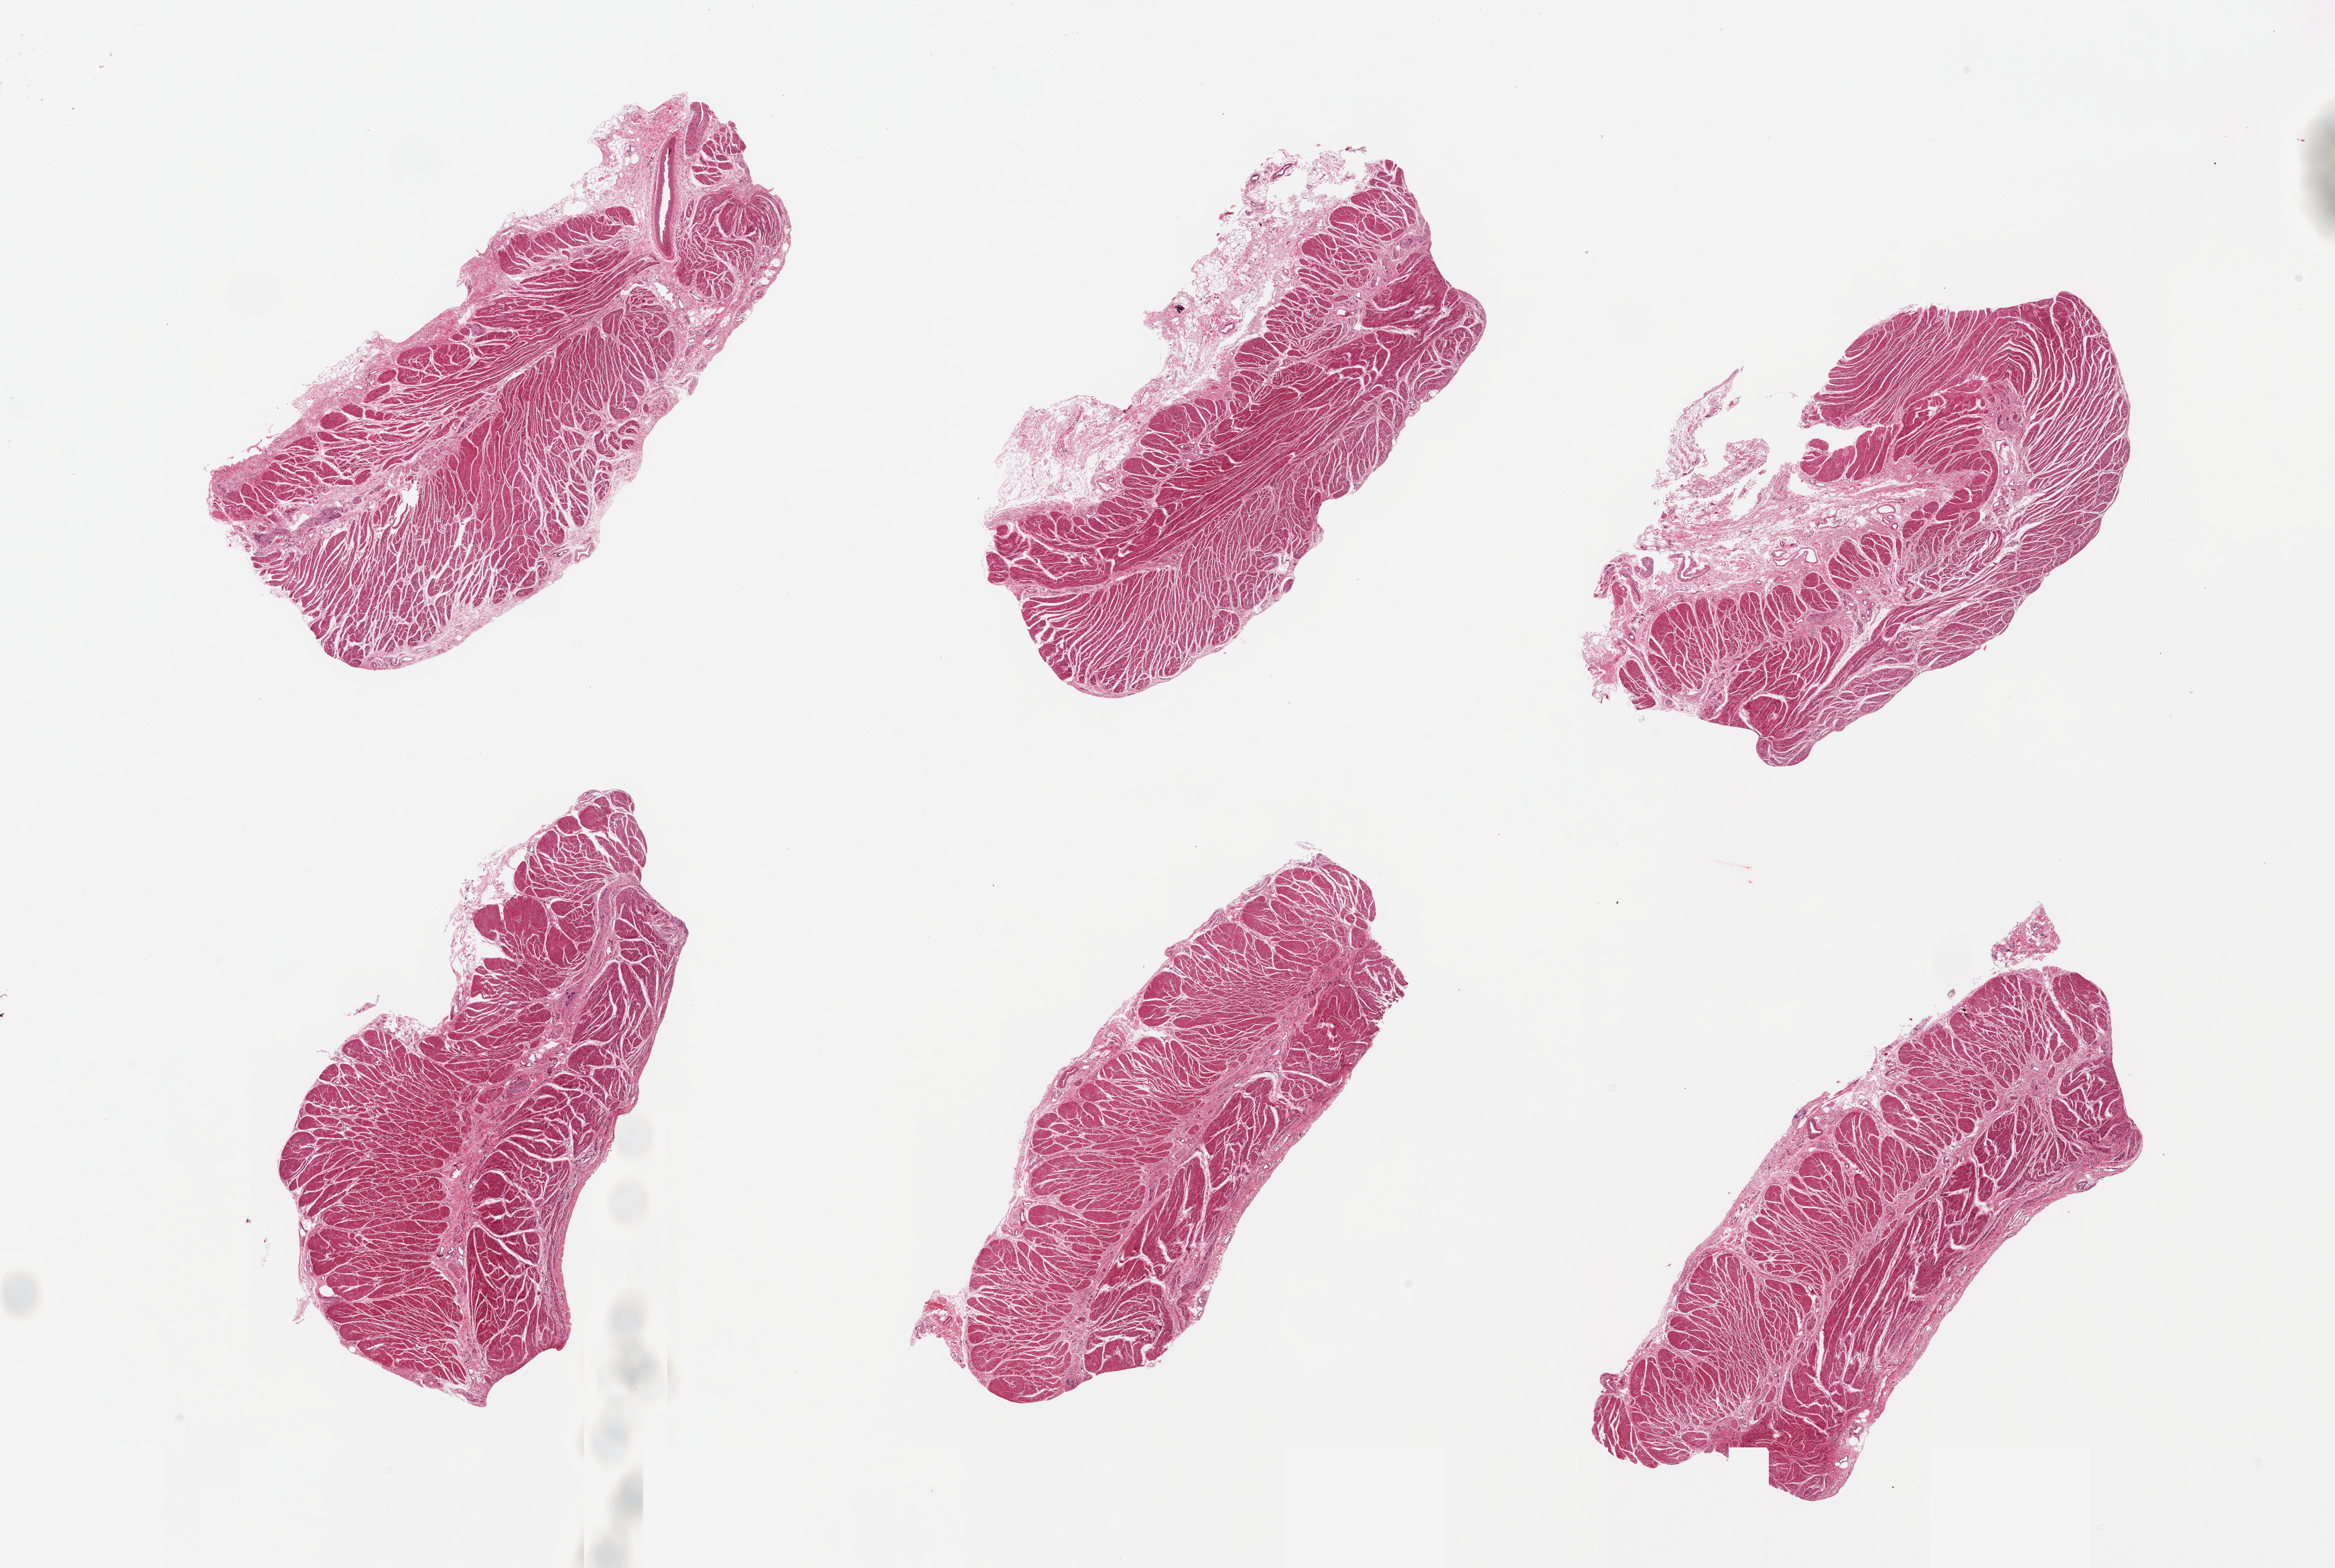
Whole-slide image, haematoxylin and eosin stain — a low-resolution overview of the entire scanned area, about 27.6 x 18.5 mm; PAXgene-fixed paraffin-embedded (PFPE) section; sampled site (target tissue): gastroesophageal junction; donor tissue sample. Donor: male.
Review note (as recorded): 6 pieces, confirmed target muscularis.